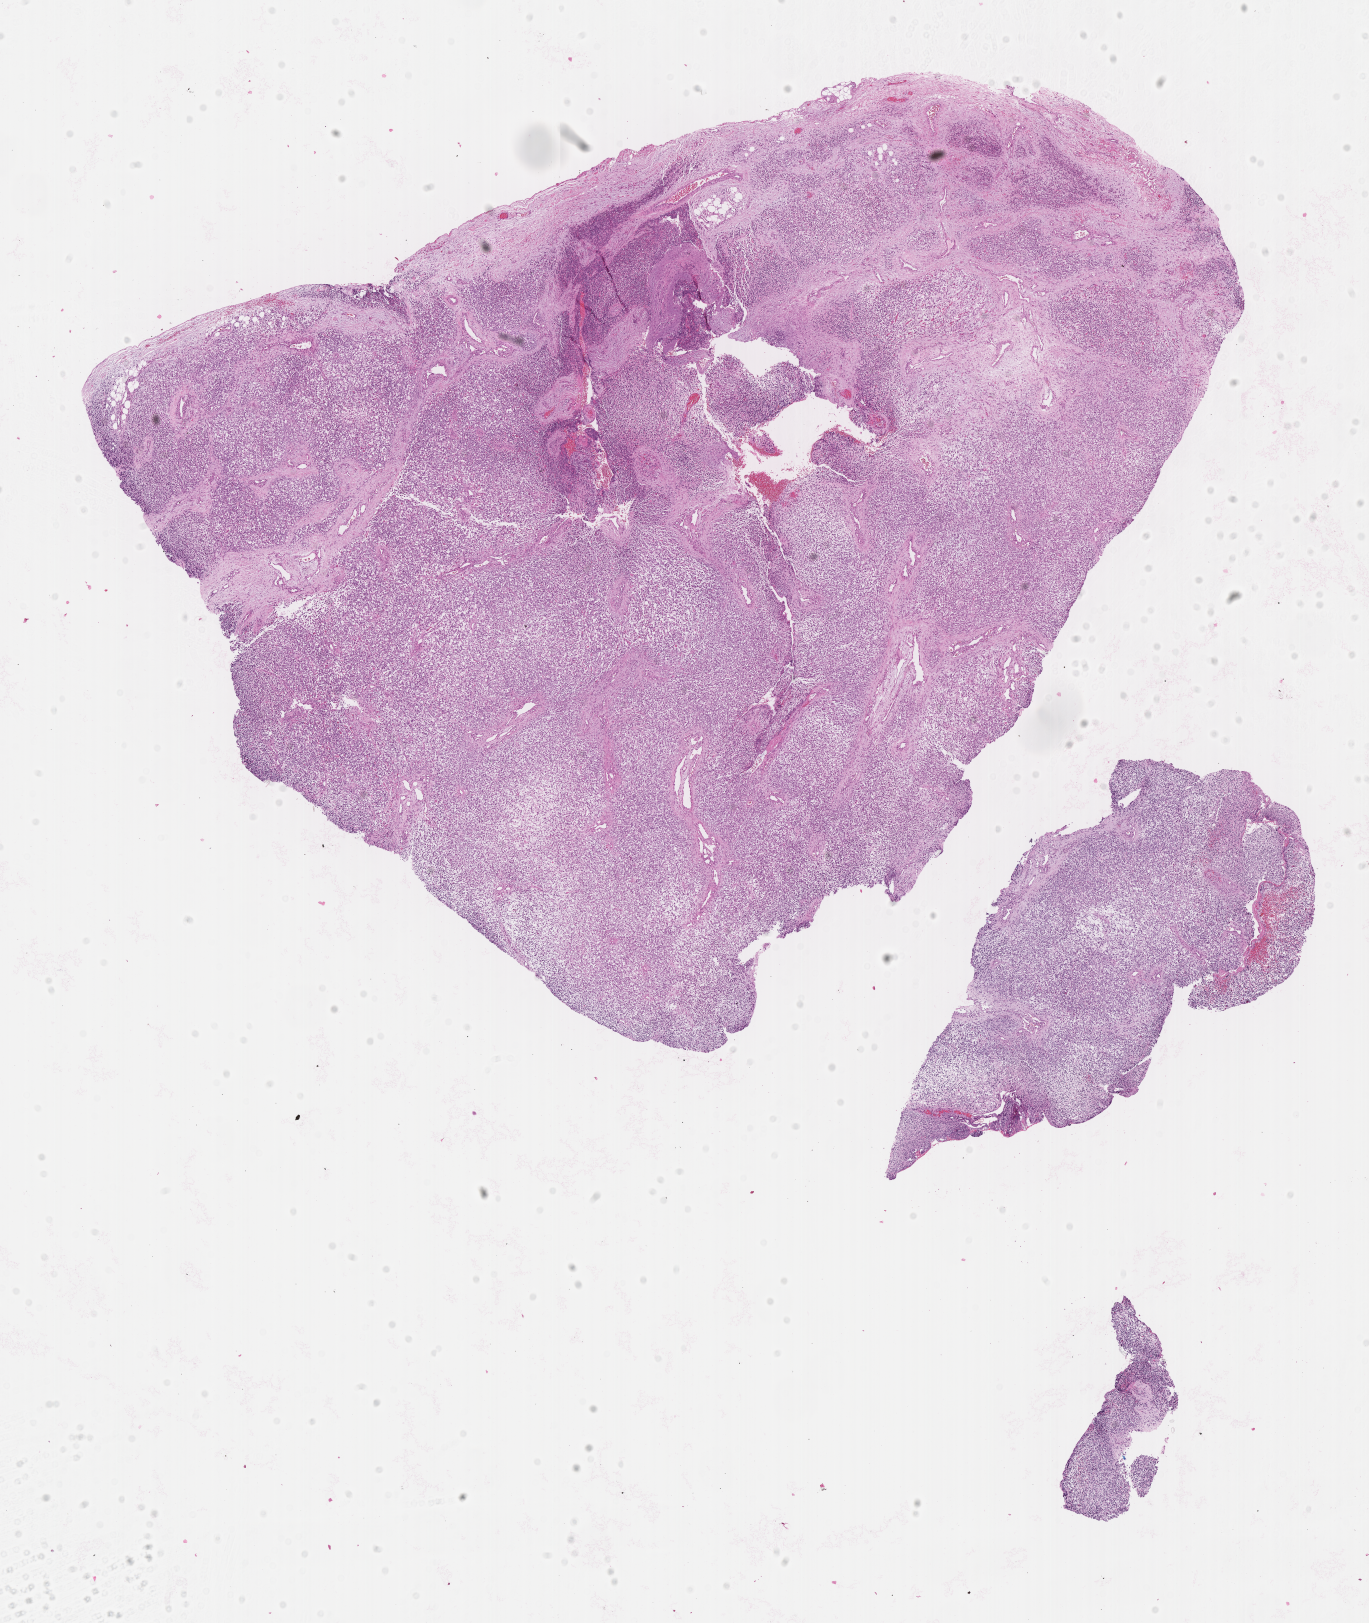
Digitized hematoxylin and eosin (H&E)-stained section of tumor tissue, a low-resolution overview of the entire scanned area, about 11.1 x 13.1 mm. FFPE section. Sample anatomic site: eye, orbit-left. Male patient, age at diagnosis 8.3 years.
Metastatic status at presentation (as recorded): non-metastatic. Diagnosis: rhabdomyosarcoma; histological classification: embryonal rhabdomyosarcoma. Stage (as recorded): 1.